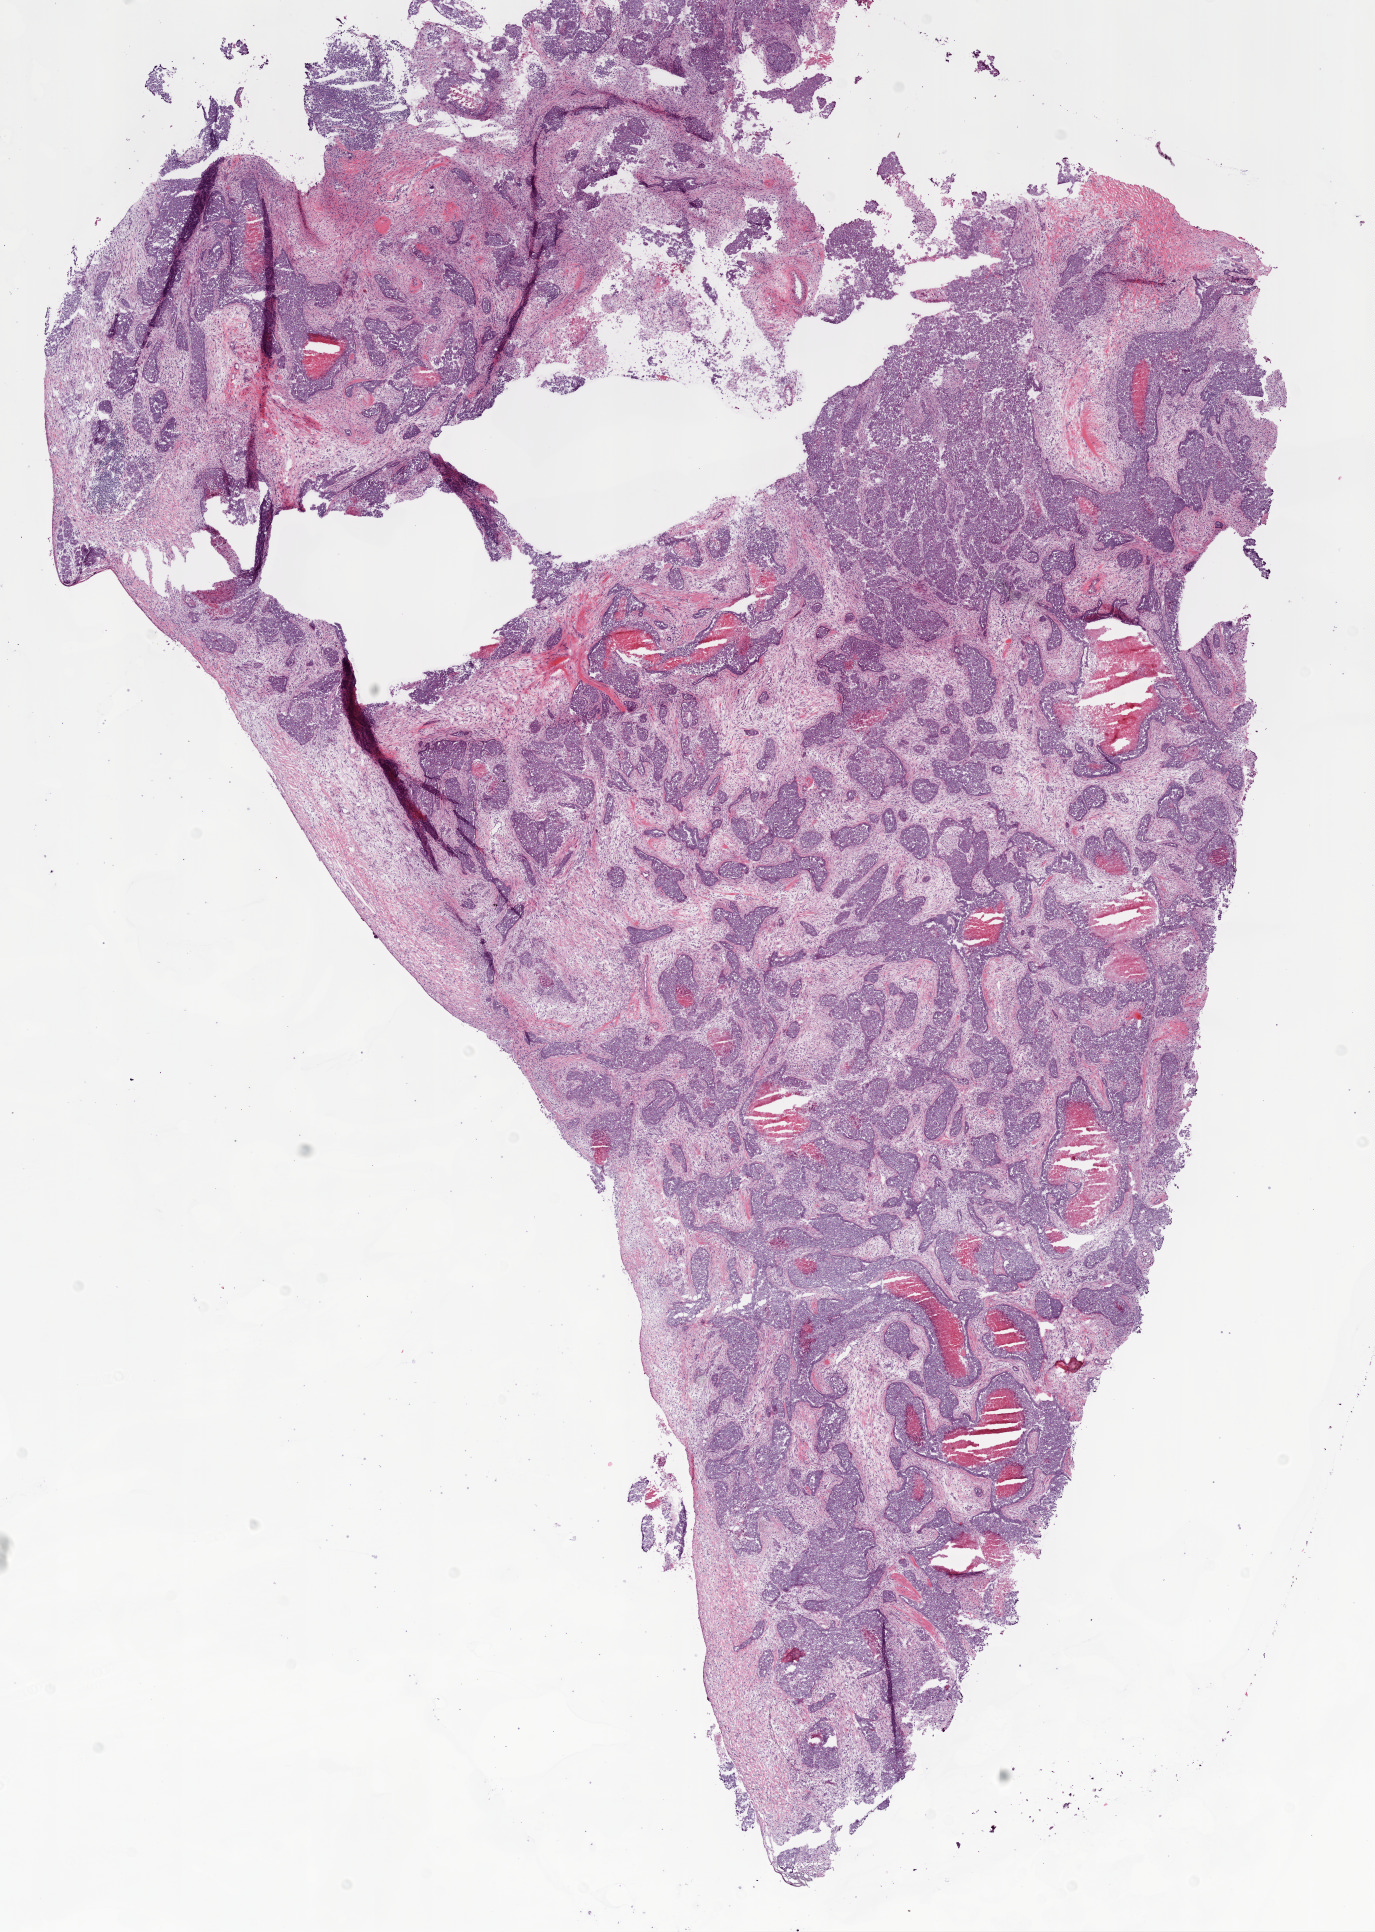
Whole-slide histology image, Hematoxylin and eosin (H&E) stained — whole scanned area (about 11.0 x 15.5 mm) shown as a low-resolution overview; frozen section from the bottom of the tissue portion; sample: primary tumour, ovary. Female patient; age at initial diagnosis 61 years. Histologic grade: G2 (moderately differentiated). Pathologist review of this section (percent, as recorded): tumour cells 65%, tumour nuclei 80%, normal cells 0%, stromal cells 20%, necrosis 15%.
FIGO stage: IIIC. Laterality: bilateral. Diagnosis: Serous cystadenocarcinoma, NOS.